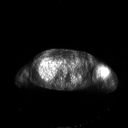
FDG PET of an extremity soft-tissue mass (from a PET/CT study), one axial slice. Slice 141 of 267 in the series (ordered by position). 3.27 mm slice thickness. 128 × 128 image matrix, field of view 700 × 700 mm. Female patient, age 83 years. From the clinical record (not read from this slice): histological type: pleiomorphic leiomyosarcoma; grade: high; site of the primary tumour: left biceps.
Annotated regions visible in this slice (expert contour drawn on MRI and transferred to this co-registered scan by the dataset authors):
- gross tumour volume including surrounding oedema: box from (x=97, y=67) to (x=108, y=76) px
- gross tumour volume (mass): (x=97, y=67)–(x=107, y=73)